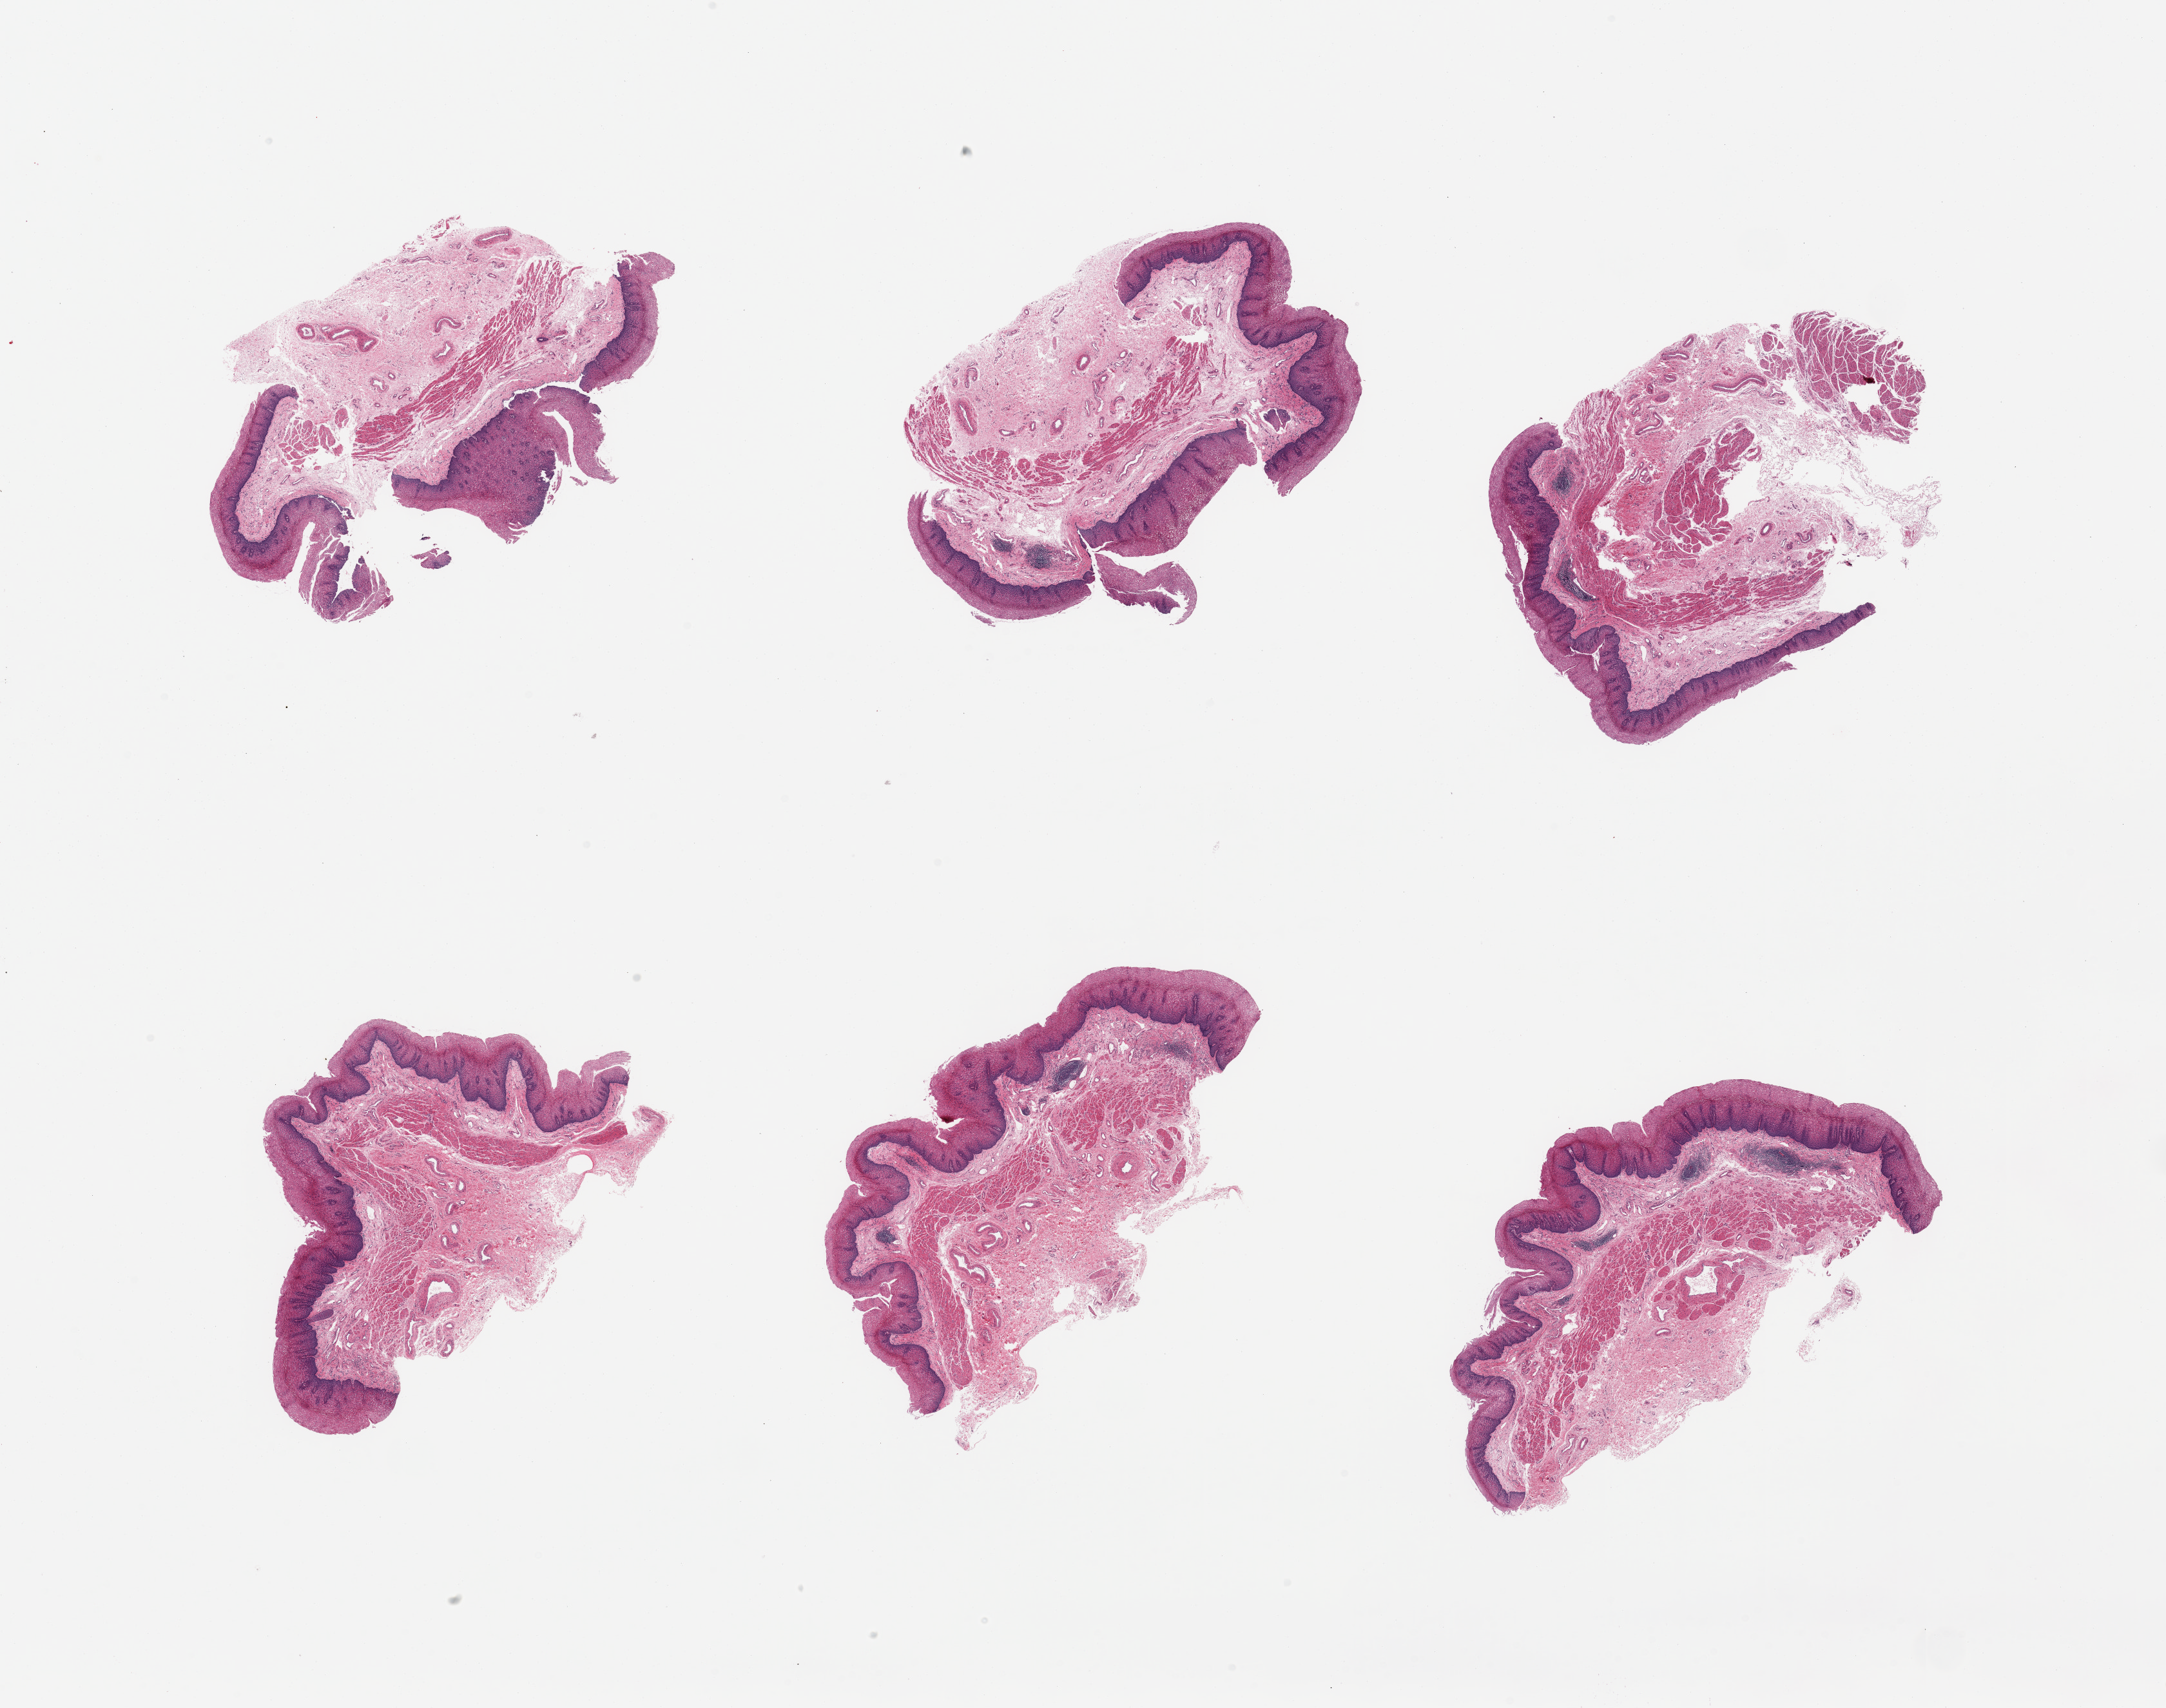
Digitized haematoxylin and eosin-stained section, whole scanned area (about 26.6 x 21.0 mm) shown as a low-resolution overview, PAXgene-fixed, paraffin-embedded tissue, sampled site (target tissue): gastroesophageal junction, tissue donor sample. Donor: male.
* reviewer comment on this tissue sample: 6 pieces; esophageal mucosa, not muscularis